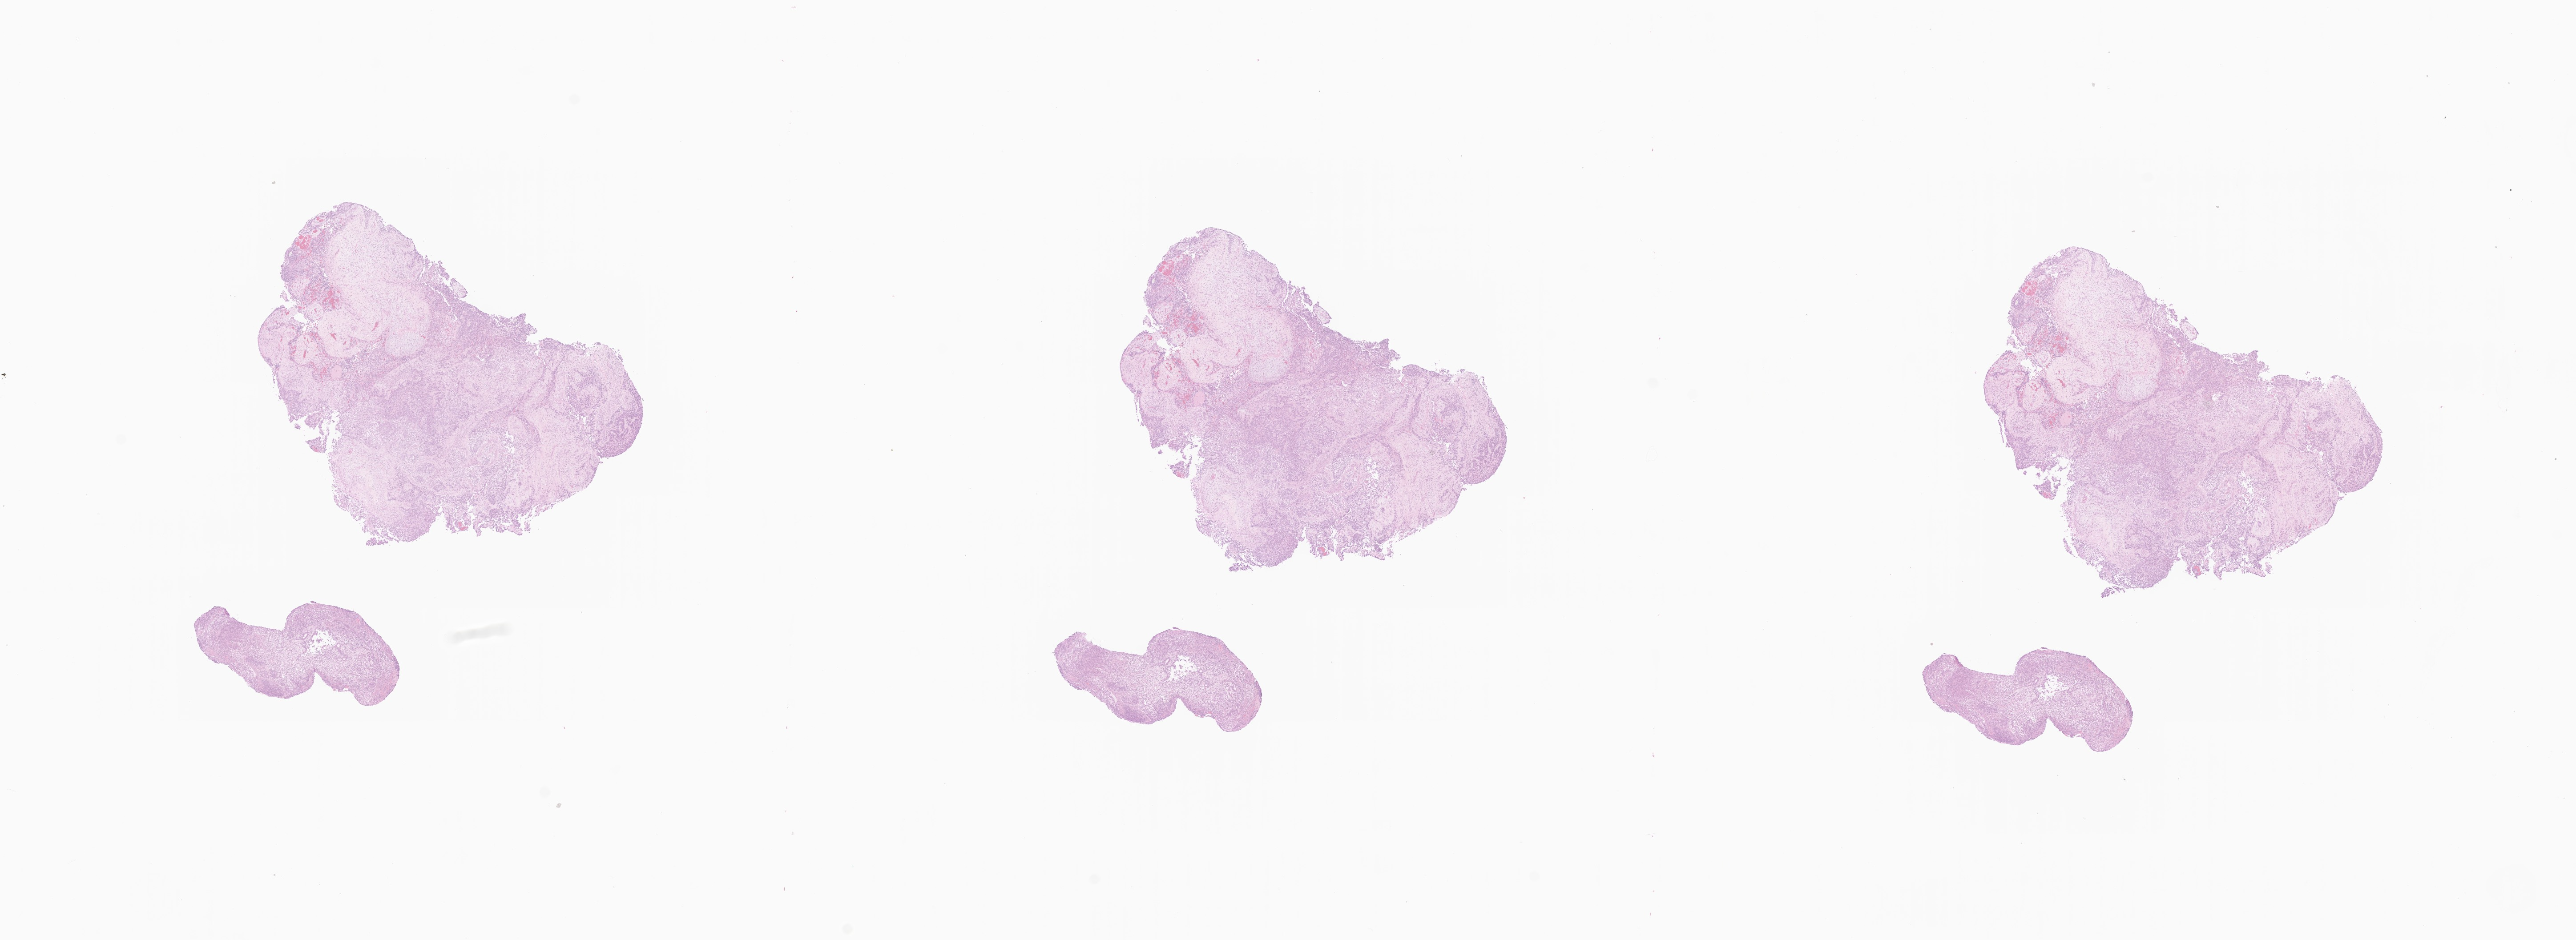
Digitized H&E-stained section of tumor tissue from the spinal cord — low-resolution overview of the scanned area, about 24.4 x 8.9 mm, formalin-fixed paraffin-embedded section. Female patient, age 153 months (12 years 9 months).
- recorded diagnosis: Medulloepithelioma, NOS